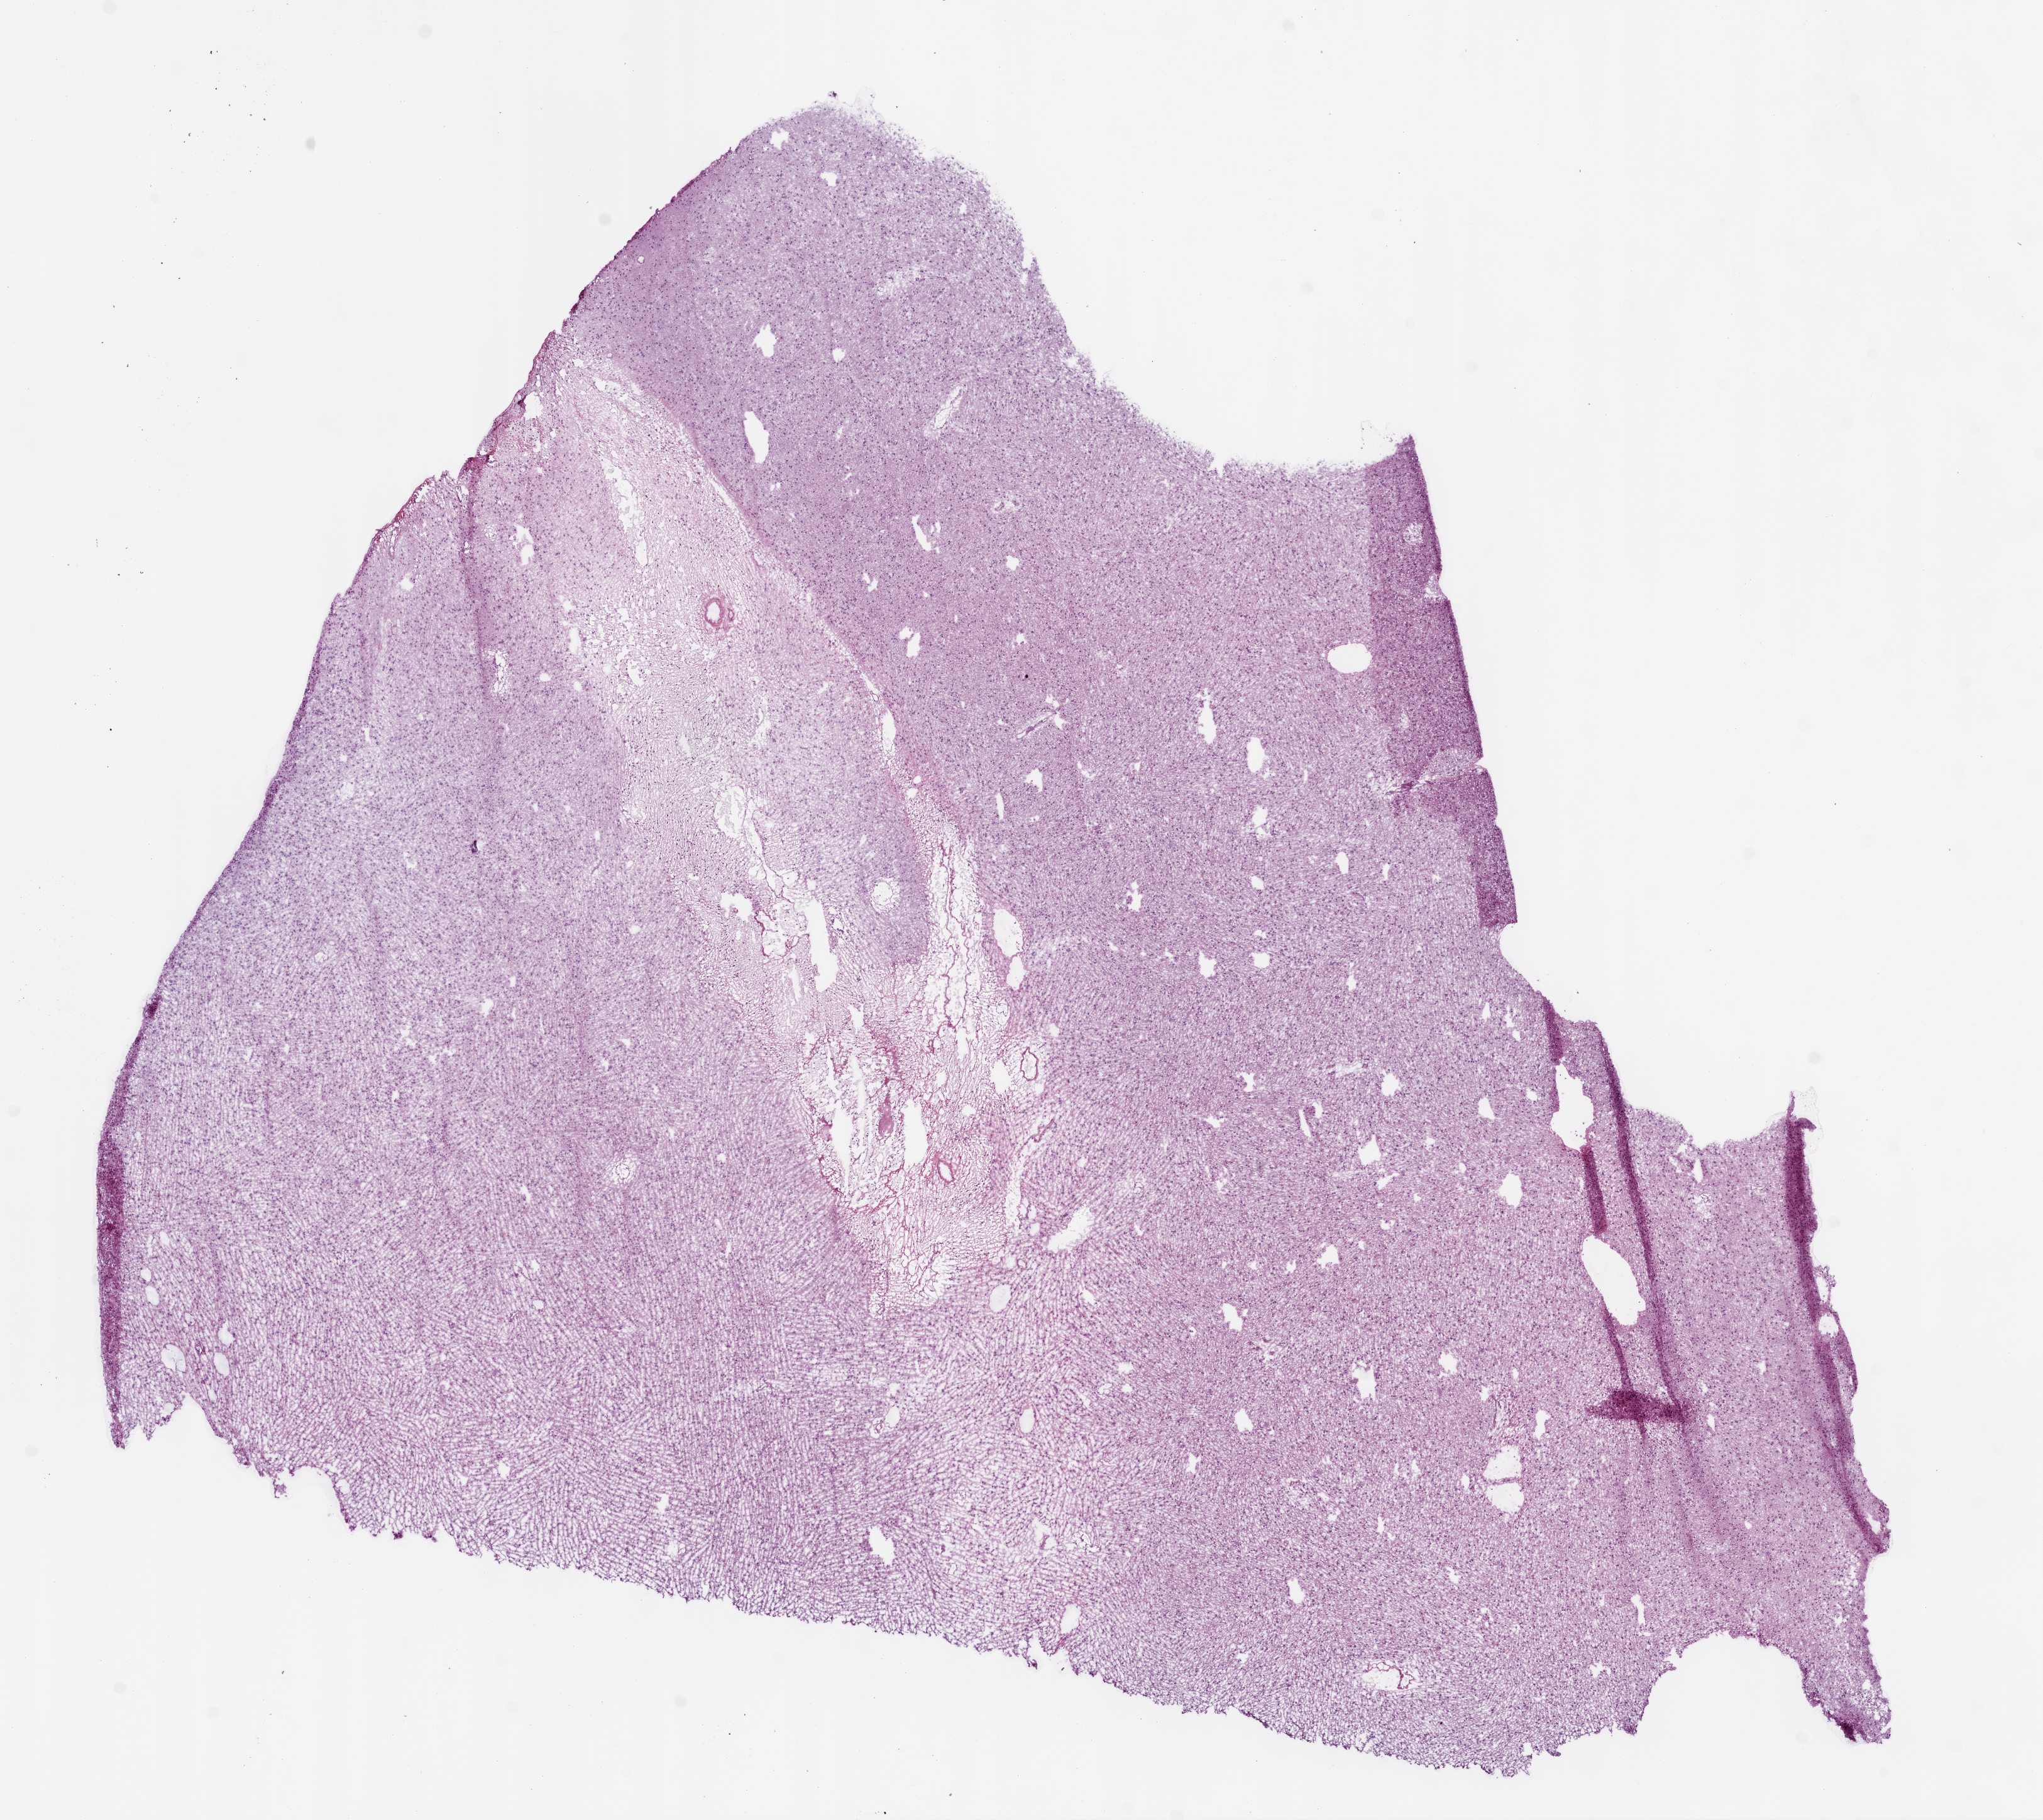
H&E whole-slide image, a low-resolution overview of the entire scanned area, about 13.0 x 11.6 mm (slide scanned at 20x), frozen section, primary tumour sample from the brain. Patient: male, age at initial diagnosis 59 years. Histologic grade: G2 (moderately differentiated). Slide review estimates, as recorded: tumour cells 100%, tumour nuclei 60%, normal cells 0%, stromal cells 0%, necrosis 0%.
Pathologic diagnosis: Oligodendroglioma, NOS (cerebrum). Laterality: right.